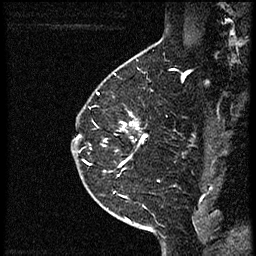
Breast MRI (dynamic contrast-enhanced), one sagittal slice; slice 42 of 56 in the series (ordered by position); dynamic contrast-enhanced study with each time point stored as its own series, time point 2 of 4 at this slice position (early post-contrast, ordered by acquisition time); 1.5 T; TE 4.2 ms, TR 18.9 ms; 2 mm slice thickness; 256 × 256 image matrix. Female patient. Case-level facts recorded for this patient, not image findings: setting: breast cancer imaged before/during neoadjuvant chemotherapy; receptor status: HER2-positive.
Outlined on this slice (semi-automatic segmentation, software-assisted and operator-edited):
- analysis volume of interest (the breast-tissue region the enhancement analysis was run in; not a lesion): bounding box [x1, y1, x2, y2] px = [78, 87, 161, 189]
- tumour enhancement mask (voxels above the 100 % enhancement threshold inside the analysis volume of interest): [106, 120, 148, 171]